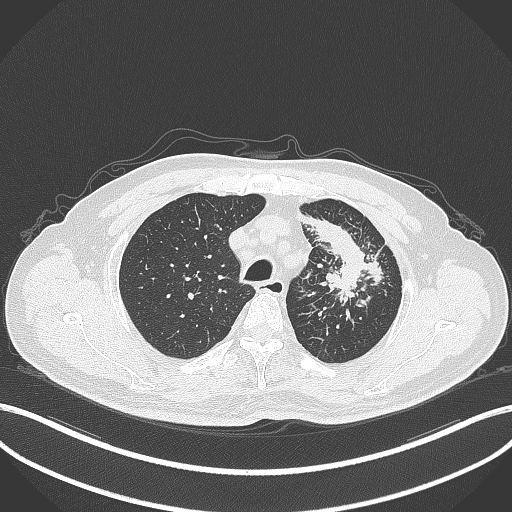
Chest CT, one axial slice. Position 283 of 386 along the scan axis. 120 kVp. Lung window (W 1500 / L -600 HU). 512 × 512 image matrix, field of view 400 × 400 mm. Patient: male, 69 years. Case-level facts recorded for this patient, not image findings: clinical TNM (as recorded): T2a N2 M0; histopathological grade: G2-3.
Annotated regions visible in this slice (rectangle marked by the reading radiologist):
- lung tumour (recorded histology: adenocarcinoma): box from (x=300, y=208) to (x=391, y=300) px